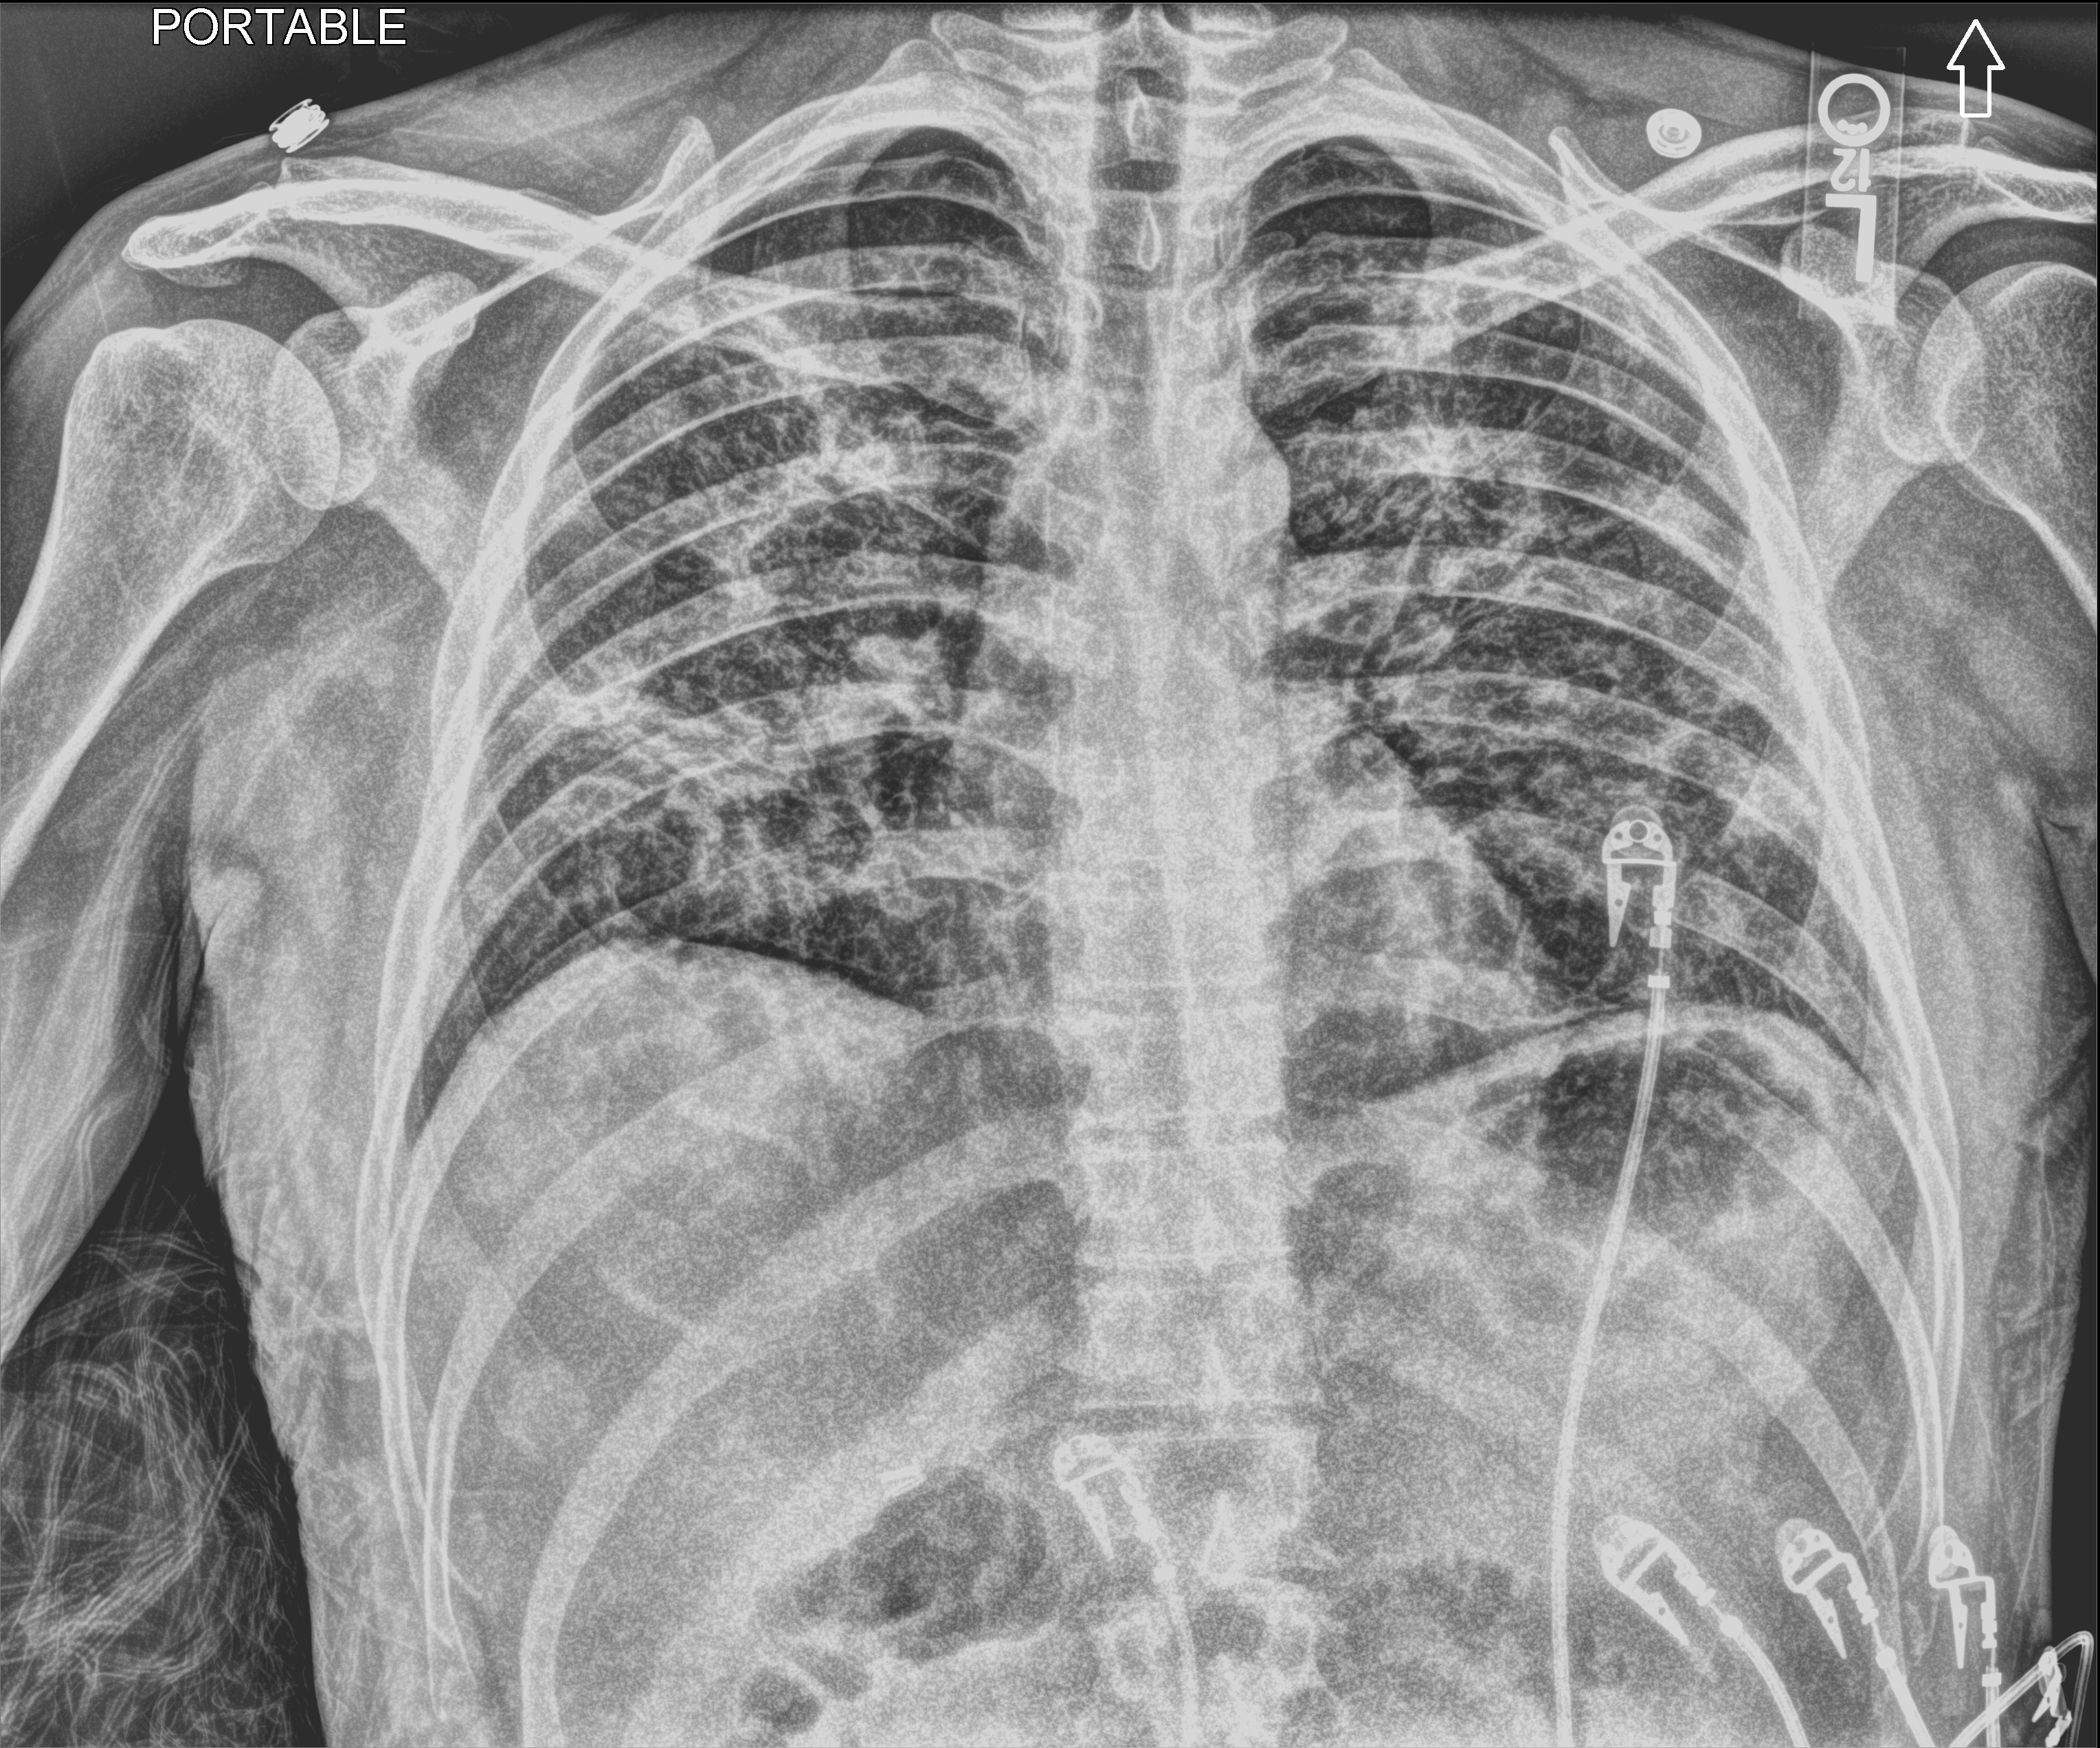
Portable chest radiograph, anteroposterior (AP) projection. Male patient hospitalised with COVID-19, age 18–59 years.
From the hospital-stay record, not from the radiograph (when in the stay this image was taken is not recorded): admitted to intensive care during this hospital stay: yes; mechanically ventilated during this hospital stay: yes.